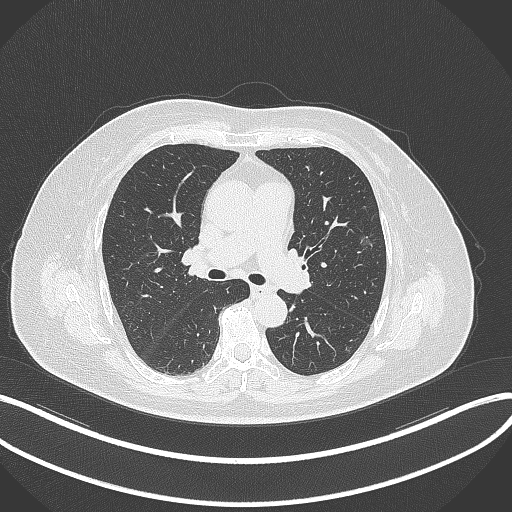
Chest CT, one axial slice. Position 217 of 315 along the scan axis. Reconstruction kernel B70f. 120 kVp. Lung window (W 1500 / L -600 HU). 512 × 512 image matrix, field of view 400 × 400 mm. Female patient, age 76 years. Case-level facts recorded for this patient, not image findings: clinical TNM (as recorded): T1b N0 M0.
Structures marked on this image (bounding box drawn by a radiologist):
- lung tumour (recorded histology: adenocarcinoma): bounding box <353,228,375,258> (left, top, right, bottom; pixels)